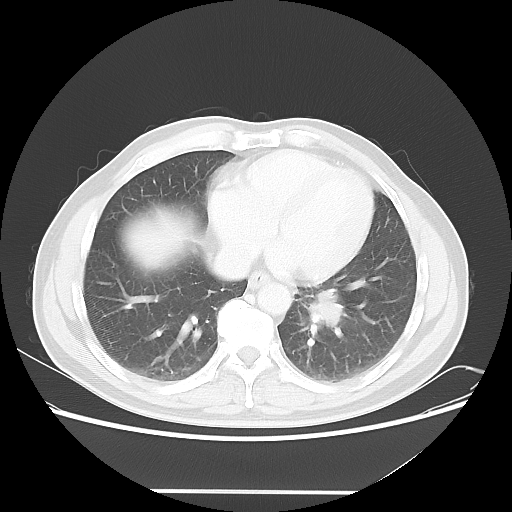
Chest CT, one axial slice; position 18 of 53 along the scan axis; 120 kVp; lung window (W 1500 / L -600 HU); 5 mm slice thickness; 512 × 512 image matrix, field of view 385 × 385 mm. Patient: male, 61 years. From the clinical record (not read from this slice): clinical TNM (as recorded): T1c N0 M0; histopathological grade: G3.
Outlined on this slice (rectangle marked by the reading radiologist):
- lung tumour (recorded histology: adenocarcinoma): box from (x=307, y=288) to (x=345, y=337) px